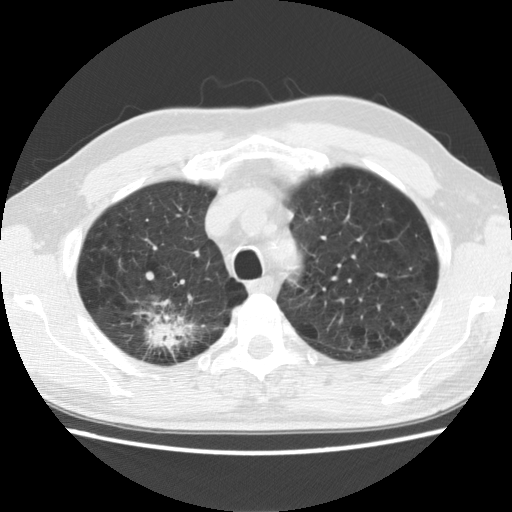
Axial slice from a low-dose chest CT screening exam, baseline screening round, lung window (W 1500 / L -600 HU), 2.5 mm slice thickness, standard (soft-tissue) reconstruction kernel (STANDARD). Male, age 64 years at enrolment. Former smoker at enrolment.
• Expert-annotated lung lesion, bounding box (x1, y1, x2, y2) in pixels: (115, 294, 204, 365).
• Reader record for this screening exam (exam-level; its link to the box is not recorded): non-calcified nodule or mass ≥4 mm, right upper lobe, 39 × 31 mm, spiculated (stellate) margins, mixed attenuation.
• Lung cancer was diagnosed 74 days after this screen: adenocarcinoma, NOS, right upper lobe, moderately differentiated (G2), stage IB (AJCC 6th edition), 40 mm at pathology.